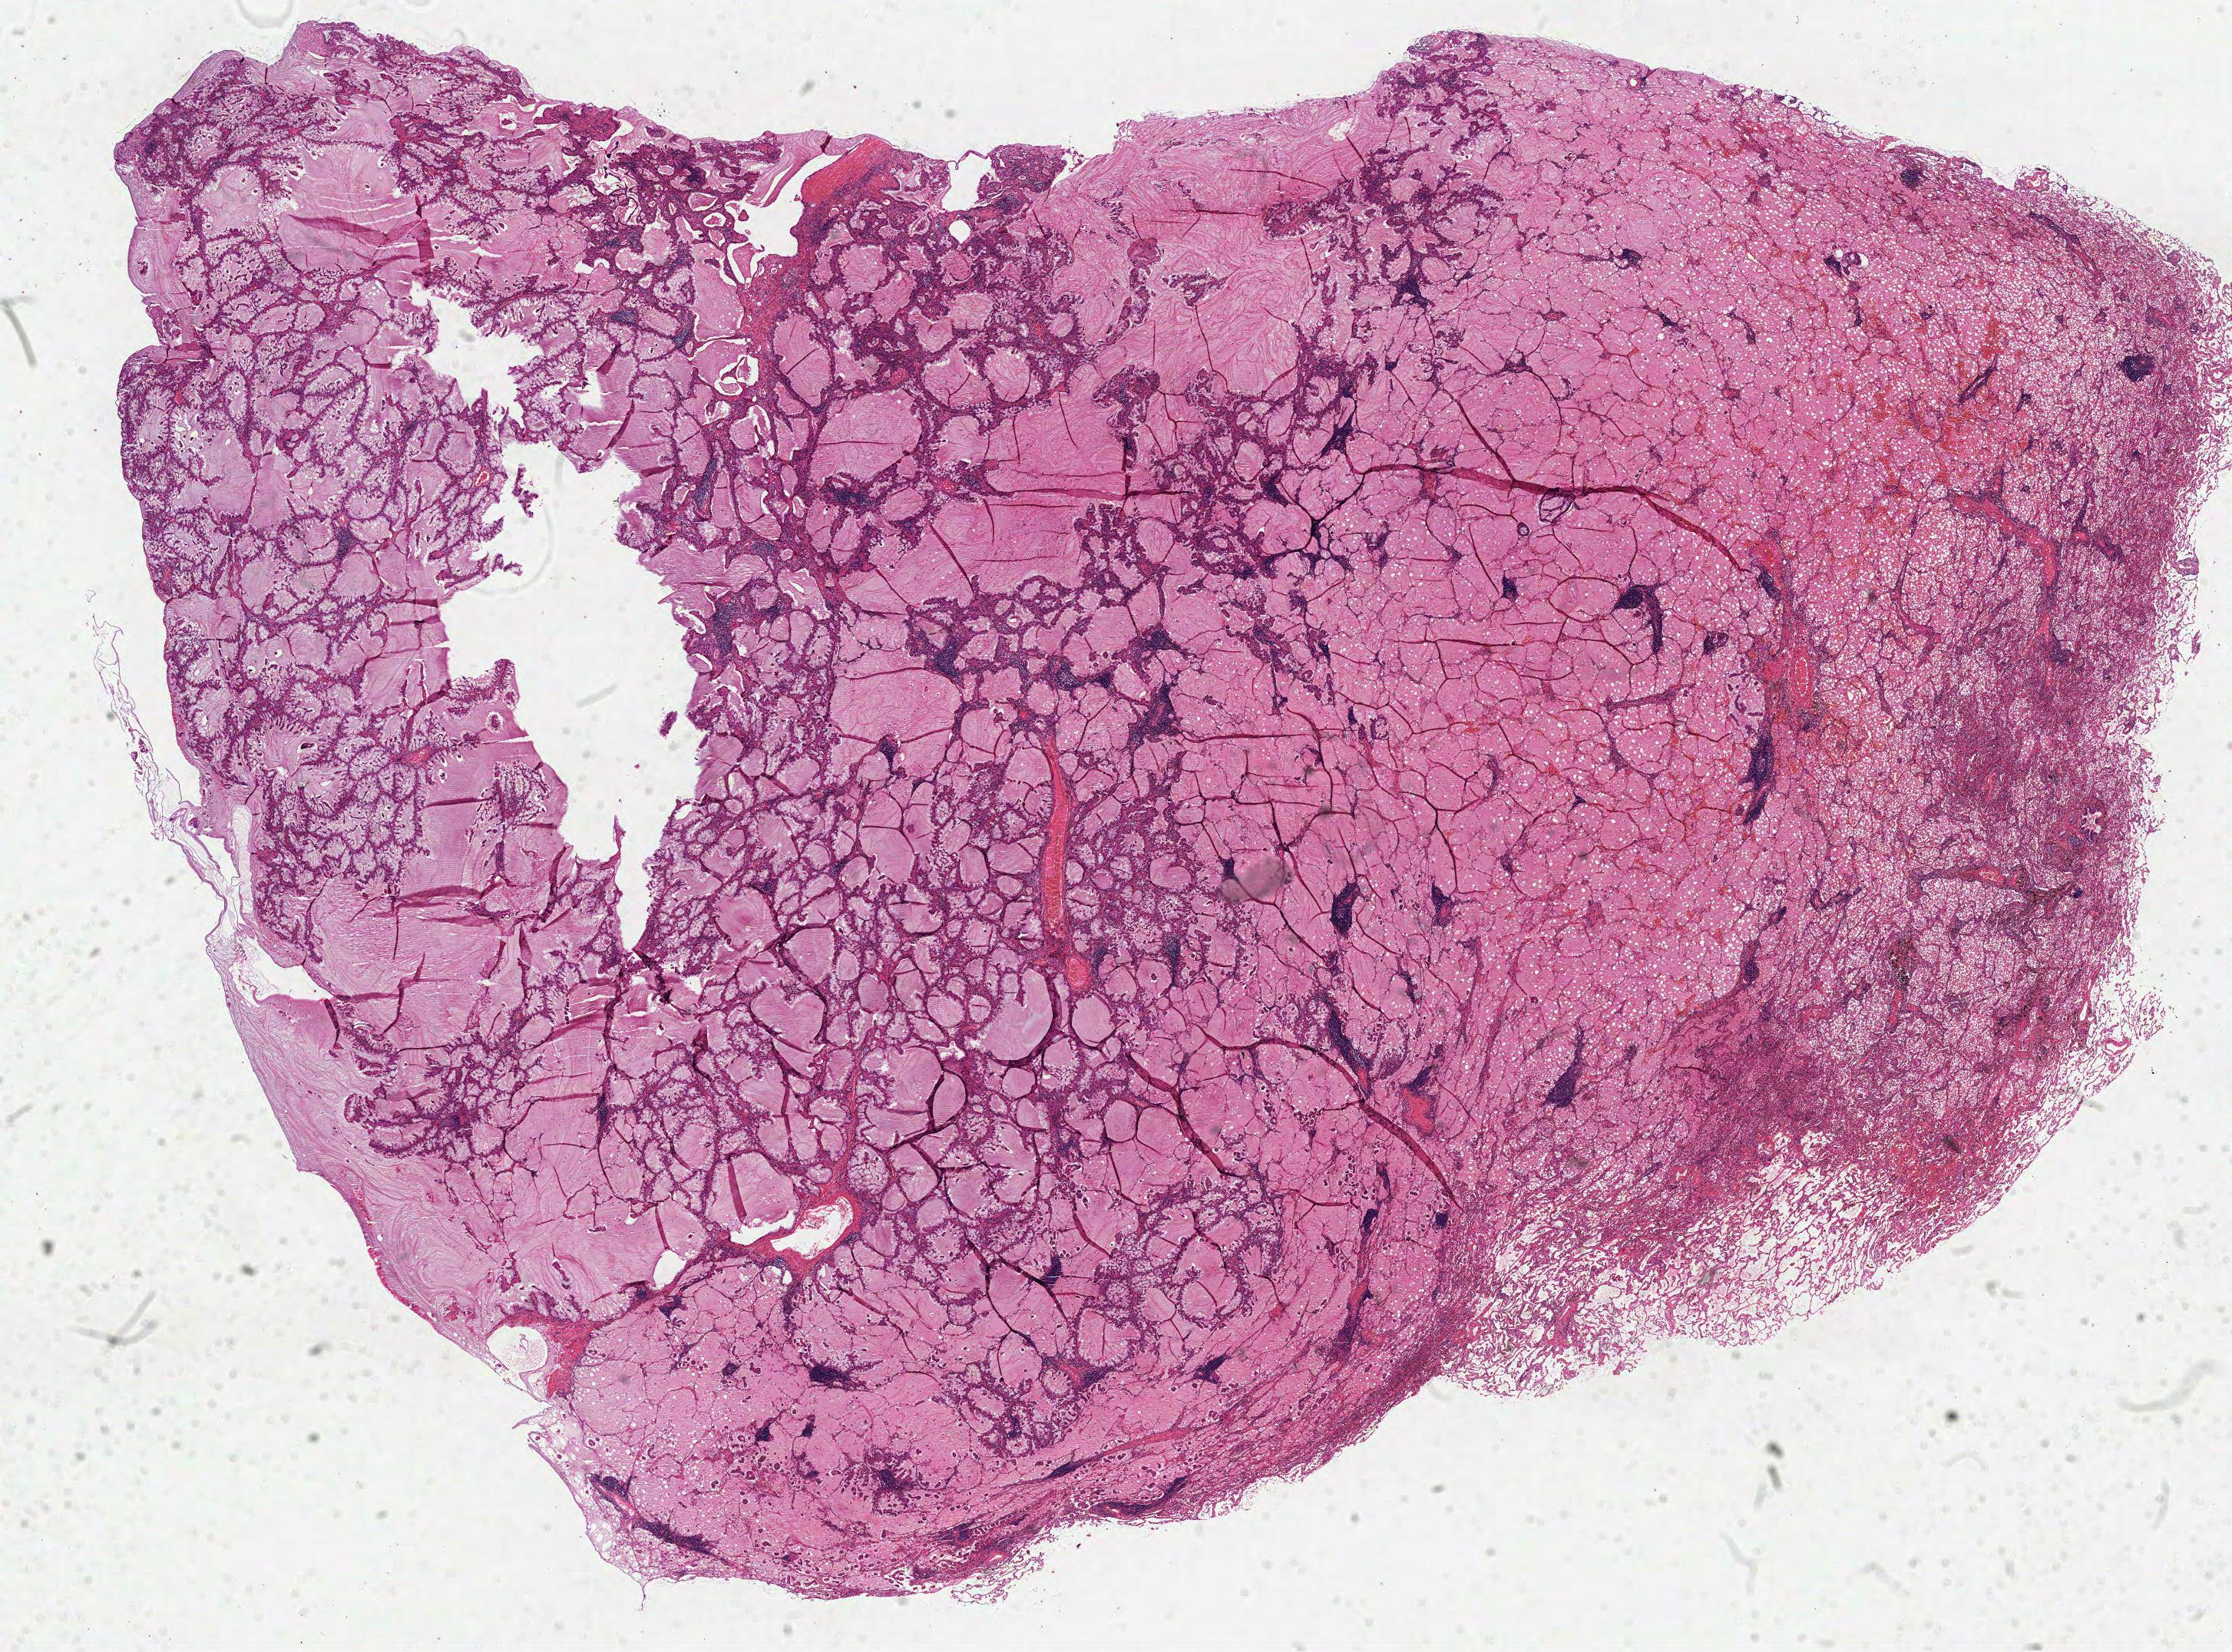
Whole-slide histology image, Hematoxylin and eosin (H&E) stained — whole scanned area (about 23.4 x 17.4 mm, acquisition: 40x scan) shown as a low-resolution overview. Formalin-fixed paraffin-embedded (FFPE) diagnostic section. Lung, primary tumour sample. Male, age 60 years at initial diagnosis.
Pathologic diagnosis: Adenocarcinoma, NOS (lower lobe, lung). AJCC pathologic stage: IB (6th edition).